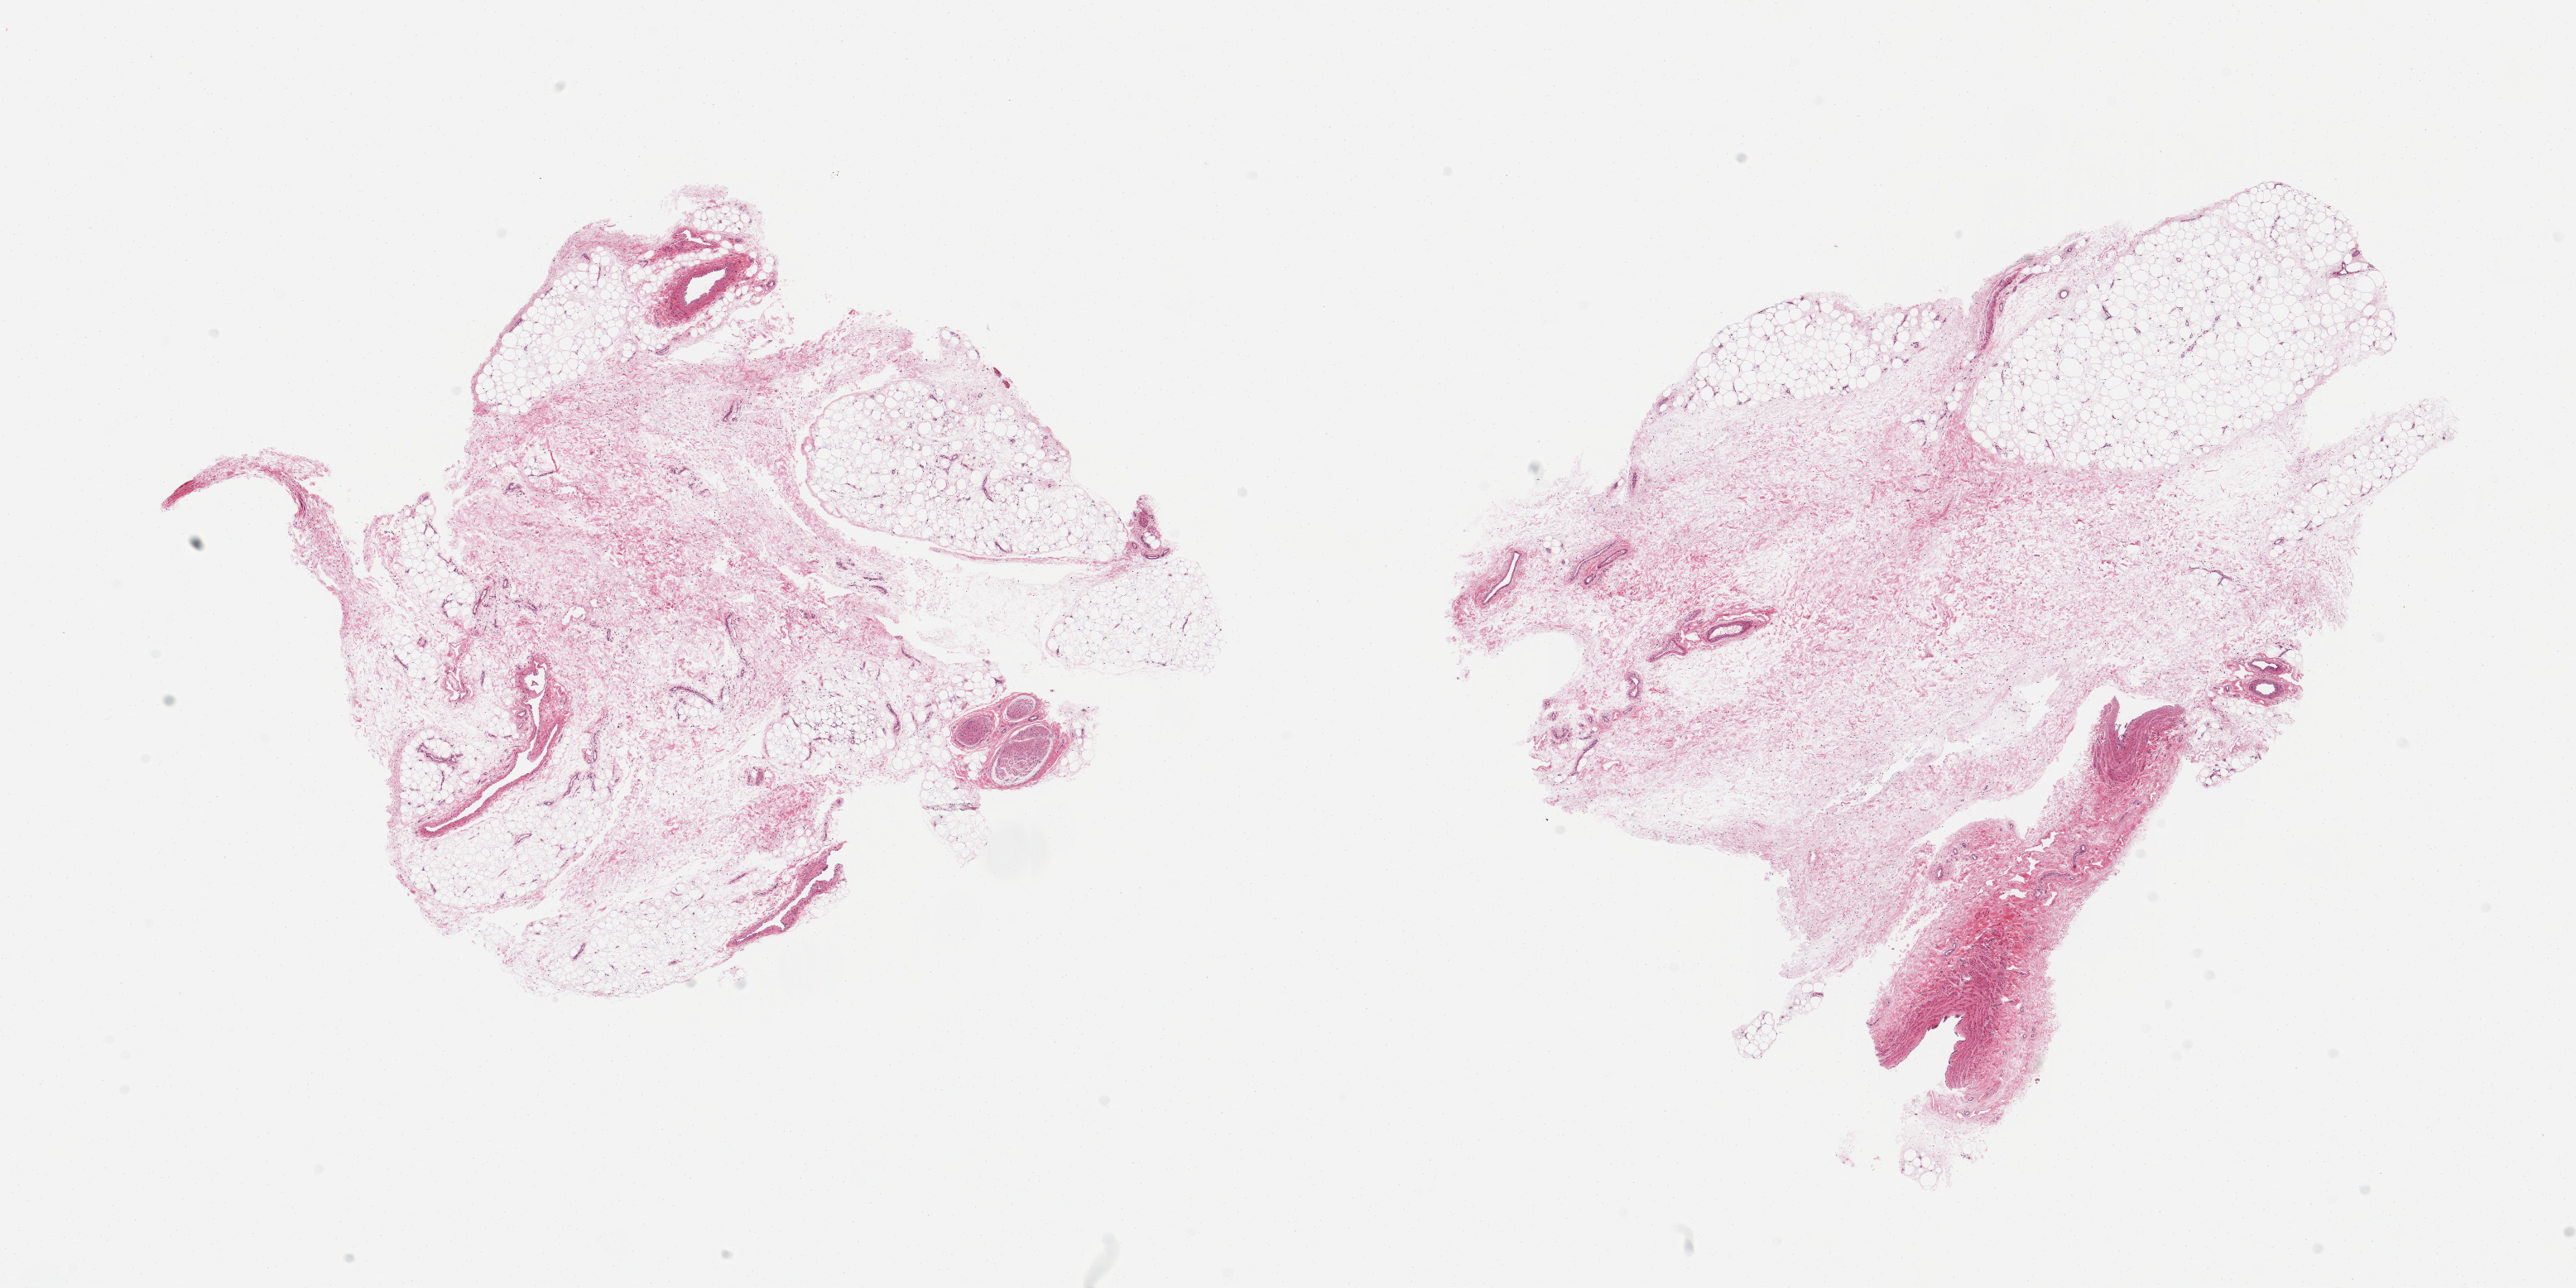
Whole-slide image, hematoxylin and eosin (H&E) stain, brightfield — low-resolution overview of the scanned area, about 24.6 x 12.3 mm (from a 20x scan). PAXgene-fixed, paraffin-embedded tissue. Target tissue: adipose tissue. Tissue donor sample. Male donor.
Reviewer comment on this tissue sample: 2 pieces; 20 and 50% fat, remainder is loose connective tissue, vessels, nerve.